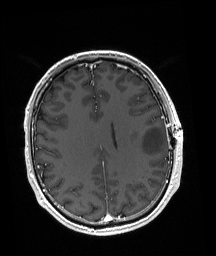
Brain MRI from a brain-tumour surgery series, one axial slice; position 72 of 192 along the scan axis; T1-weighted post-contrast; 1 mm slice thickness; 216 × 256 image matrix, field of view 211 × 250 mm. From the clinical record (not read from this slice): histopathology: Astrocytoma; WHO grade: 3; IDH mutation: yes; tumour location: Left Posterior Frontal.
Annotated regions visible in this slice (outlined manually by an expert reader):
- tumour: box from (x=140, y=126) to (x=166, y=155) px